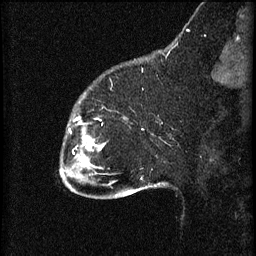
Breast MRI (dynamic contrast-enhanced), one sagittal slice; position 13 of 60 along the scan axis; 3 images stored at this slice position (order not interpretable as contrast timing); 1.5 T; TE 4.2 ms, TR 8.2 ms; 2 mm slice thickness; 256 × 256 image matrix. Female patient, age 32 years.
Annotated regions visible in this slice (semi-automatically segmented with operator editing):
- analysis volume of interest (the breast-tissue region the enhancement analysis was run in; not a lesion): bounding box (x1, y1, x2, y2) in pixels: (61, 108, 107, 165)
- tumour enhancement mask (voxels above the 70 % enhancement threshold inside the analysis volume of interest): (81, 138, 100, 165)